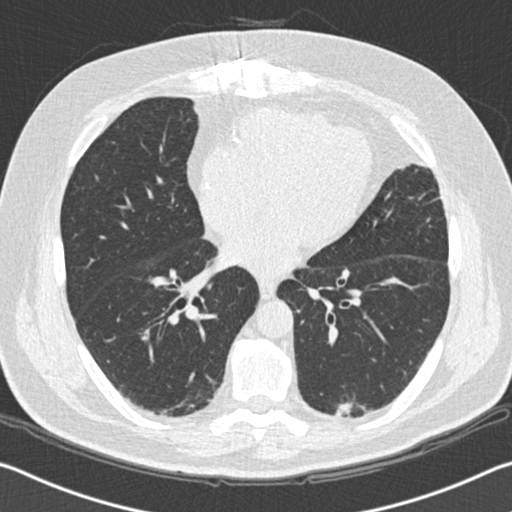
Low-dose screening chest CT, one axial slice. Position 78 of 172 along the scan axis. 120 kVp. Lung window (W 1500 / L -600 HU). 2 mm slice thickness. 512 × 512 image matrix, field of view 340 × 340 mm.
Structures marked on this image (manually delineated by an expert):
- lesion 1 (tumor, lower lobe of left lung): bounding box <336,402,367,418> (left, top, right, bottom; pixels)